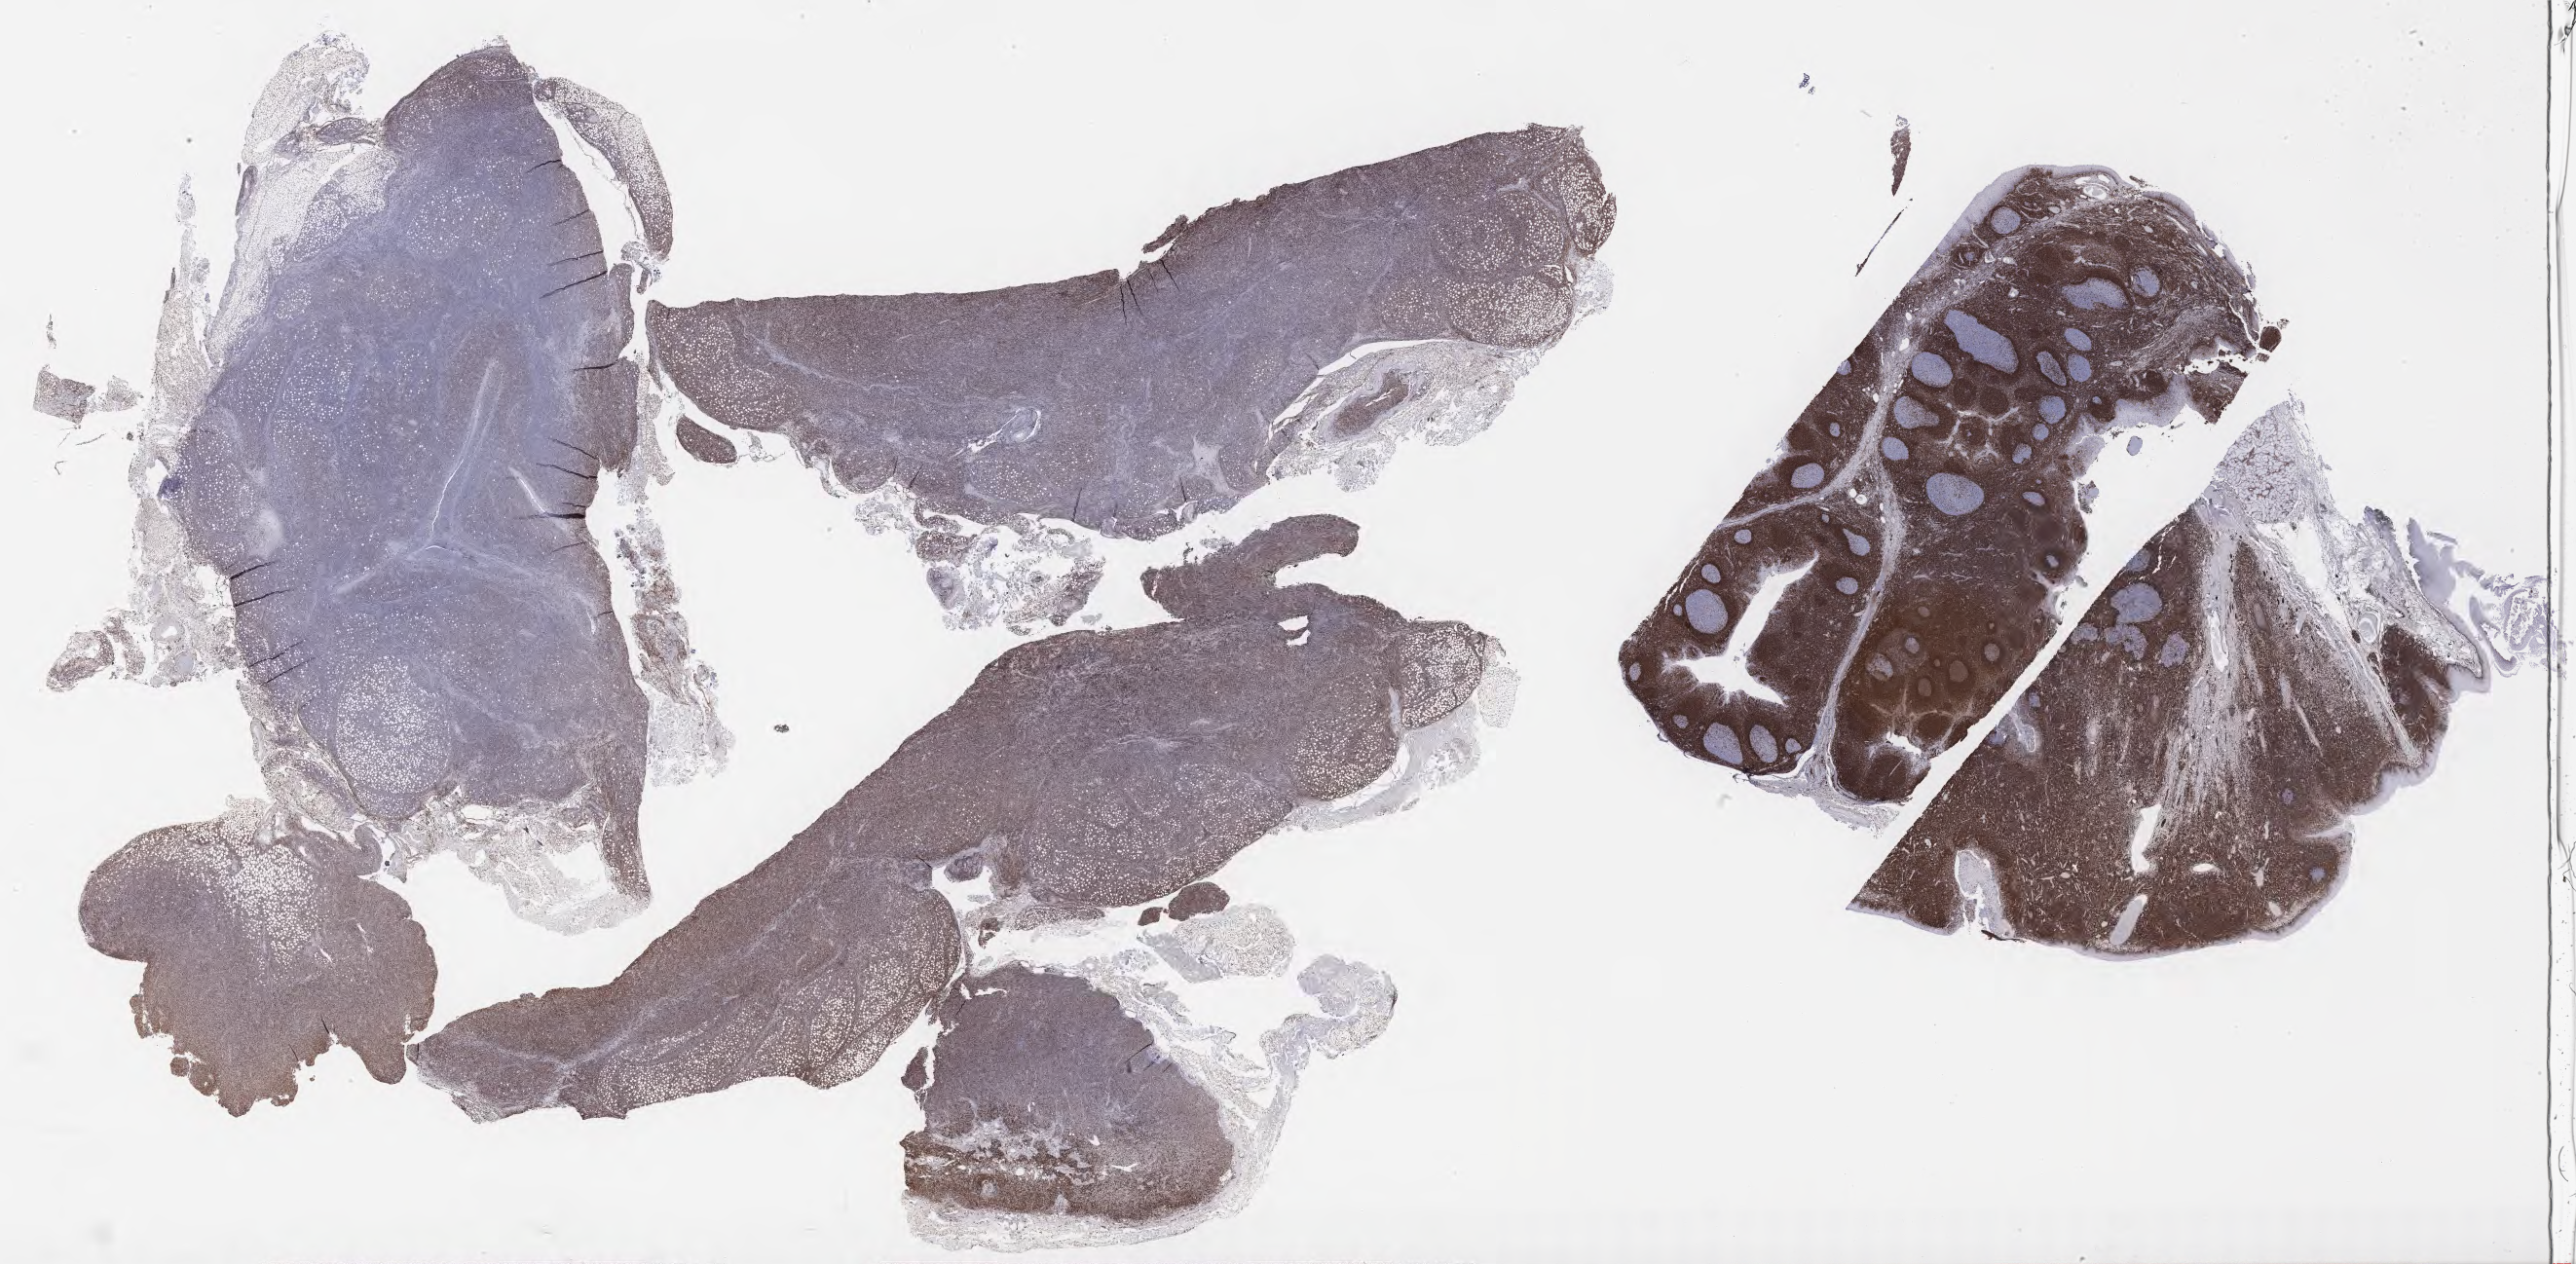
Immunohistochemistry (IHC) whole-slide image stained for BCL2 — shown as a low-resolution overview of the whole scanned area (about 42.8 x 21.0 mm); tumor tissue; anatomic site: lymph node. Patient: male, age 68 years.
* histologic diagnosis: Diffuse large B-cell lymphoma, NOS